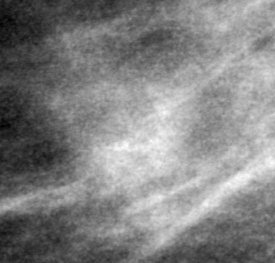
Region of interest cut from a scanned film mammogram (one marked finding); left breast; MLO view.
Mass, shape oval, margins ill defined; BI-RADS assessment category 5; pathology result (as recorded, not read from the image): malignant.